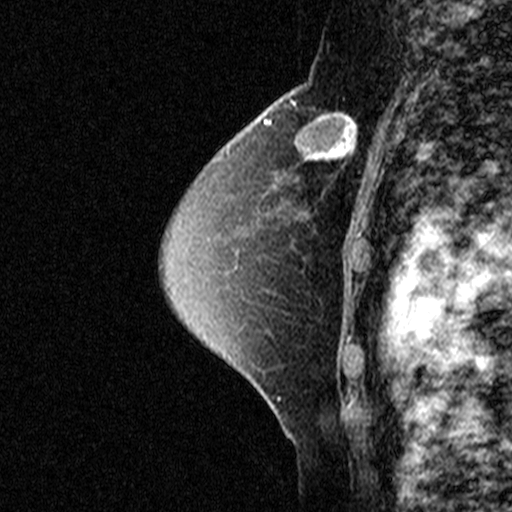
Breast MRI (dynamic contrast-enhanced), one sagittal slice; position 28 of 44 along the scan axis; dynamic contrast-enhanced study with each time point stored as its own series, time point 2 of 3 at this slice position (early post-contrast, ordered by acquisition time); 1.5 T; TE 4.5 ms, TR 11 ms; 3 mm slice thickness; 512 × 512 image matrix. Female patient, age 49 years. Case-level facts recorded for this patient, not image findings: setting: breast cancer imaged before/during neoadjuvant chemotherapy; receptor status: triple-negative.
Outlined on this slice (semi-automatically segmented with operator editing):
- analysis volume of interest (the breast-tissue region the enhancement analysis was run in; not a lesion): bounding box <276,94,369,181> (left, top, right, bottom; pixels)
- tumour enhancement mask (voxels above the 90 % enhancement threshold inside the analysis volume of interest): <294,104,357,160>